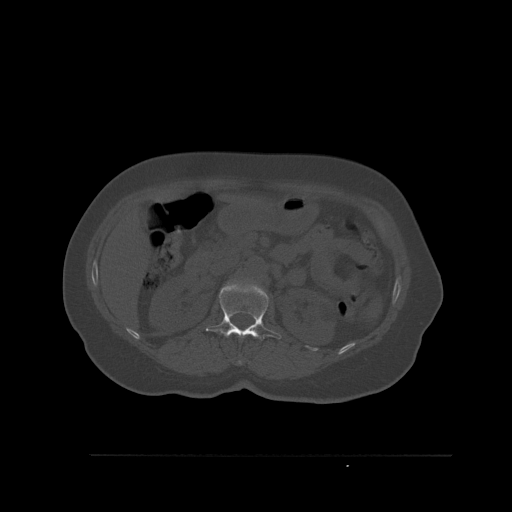
CT including the spine, one axial slice. Position 265 of 527 along the scan axis. Bone window (W 1800 / L 400 HU). 1.5 mm slice thickness. 512 × 512 image matrix, field of view 470 × 470 mm. Patient: female, 73 years. Case-level facts recorded for this patient, not image findings: primary cancer: breast; vertebrae with lytic lesions (as recorded): L2.
Annotated regions visible in this slice (semi-automatically segmented with operator editing):
- L1 vertebra: box from (x=206, y=282) to (x=281, y=341) px
- T12 vertebra: (x=237, y=360)–(x=242, y=365)